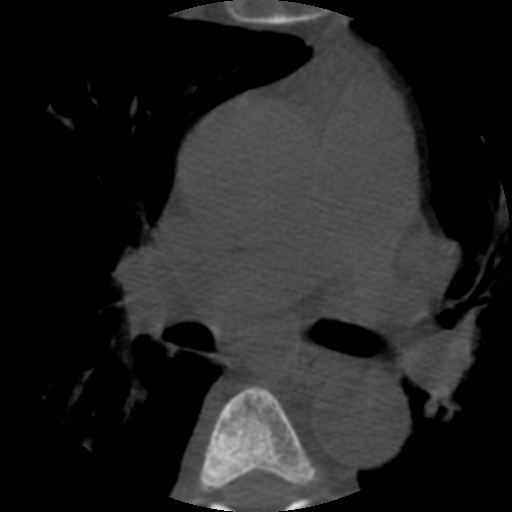
CT including the spine, one axial slice; slice 370 of 508 in the series (ordered by position); bone window (W 1800 / L 400 HU); 1.25 mm slice thickness; 512 × 512 image matrix, field of view 160 × 160 mm. Patient age 57 years. Case-level facts recorded for this patient, not image findings: primary cancer: prostate.
Outlined on this slice (semi-automatic segmentation, software-assisted and operator-edited):
- T5 vertebra: bounding box <198,387,318,491> (left, top, right, bottom; pixels)
- T6 vertebra: <209,496,312,512>